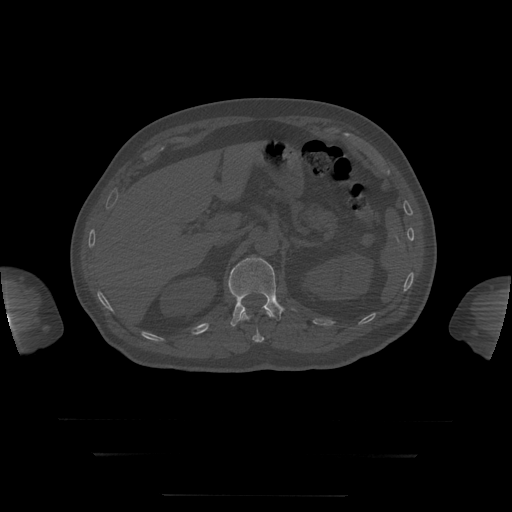
CT including the spine, one axial slice. Position 58 of 397 along the scan axis. Reconstruction kernel STANDARD. Bone window (W 1800 / L 400 HU). 1.25 mm slice thickness. 512 × 512 image matrix, field of view 510 × 510 mm. Patient age 73 years. From the clinical record (not read from this slice): primary cancer: prostate.
Annotated regions visible in this slice (semi-automatic segmentation, software-assisted and operator-edited):
- L1 vertebra: bounding box <228,257,284,327> (left, top, right, bottom; pixels)
- T12 vertebra: <240,312,271,343>
- T8 vertebra: <242,307,272,315>